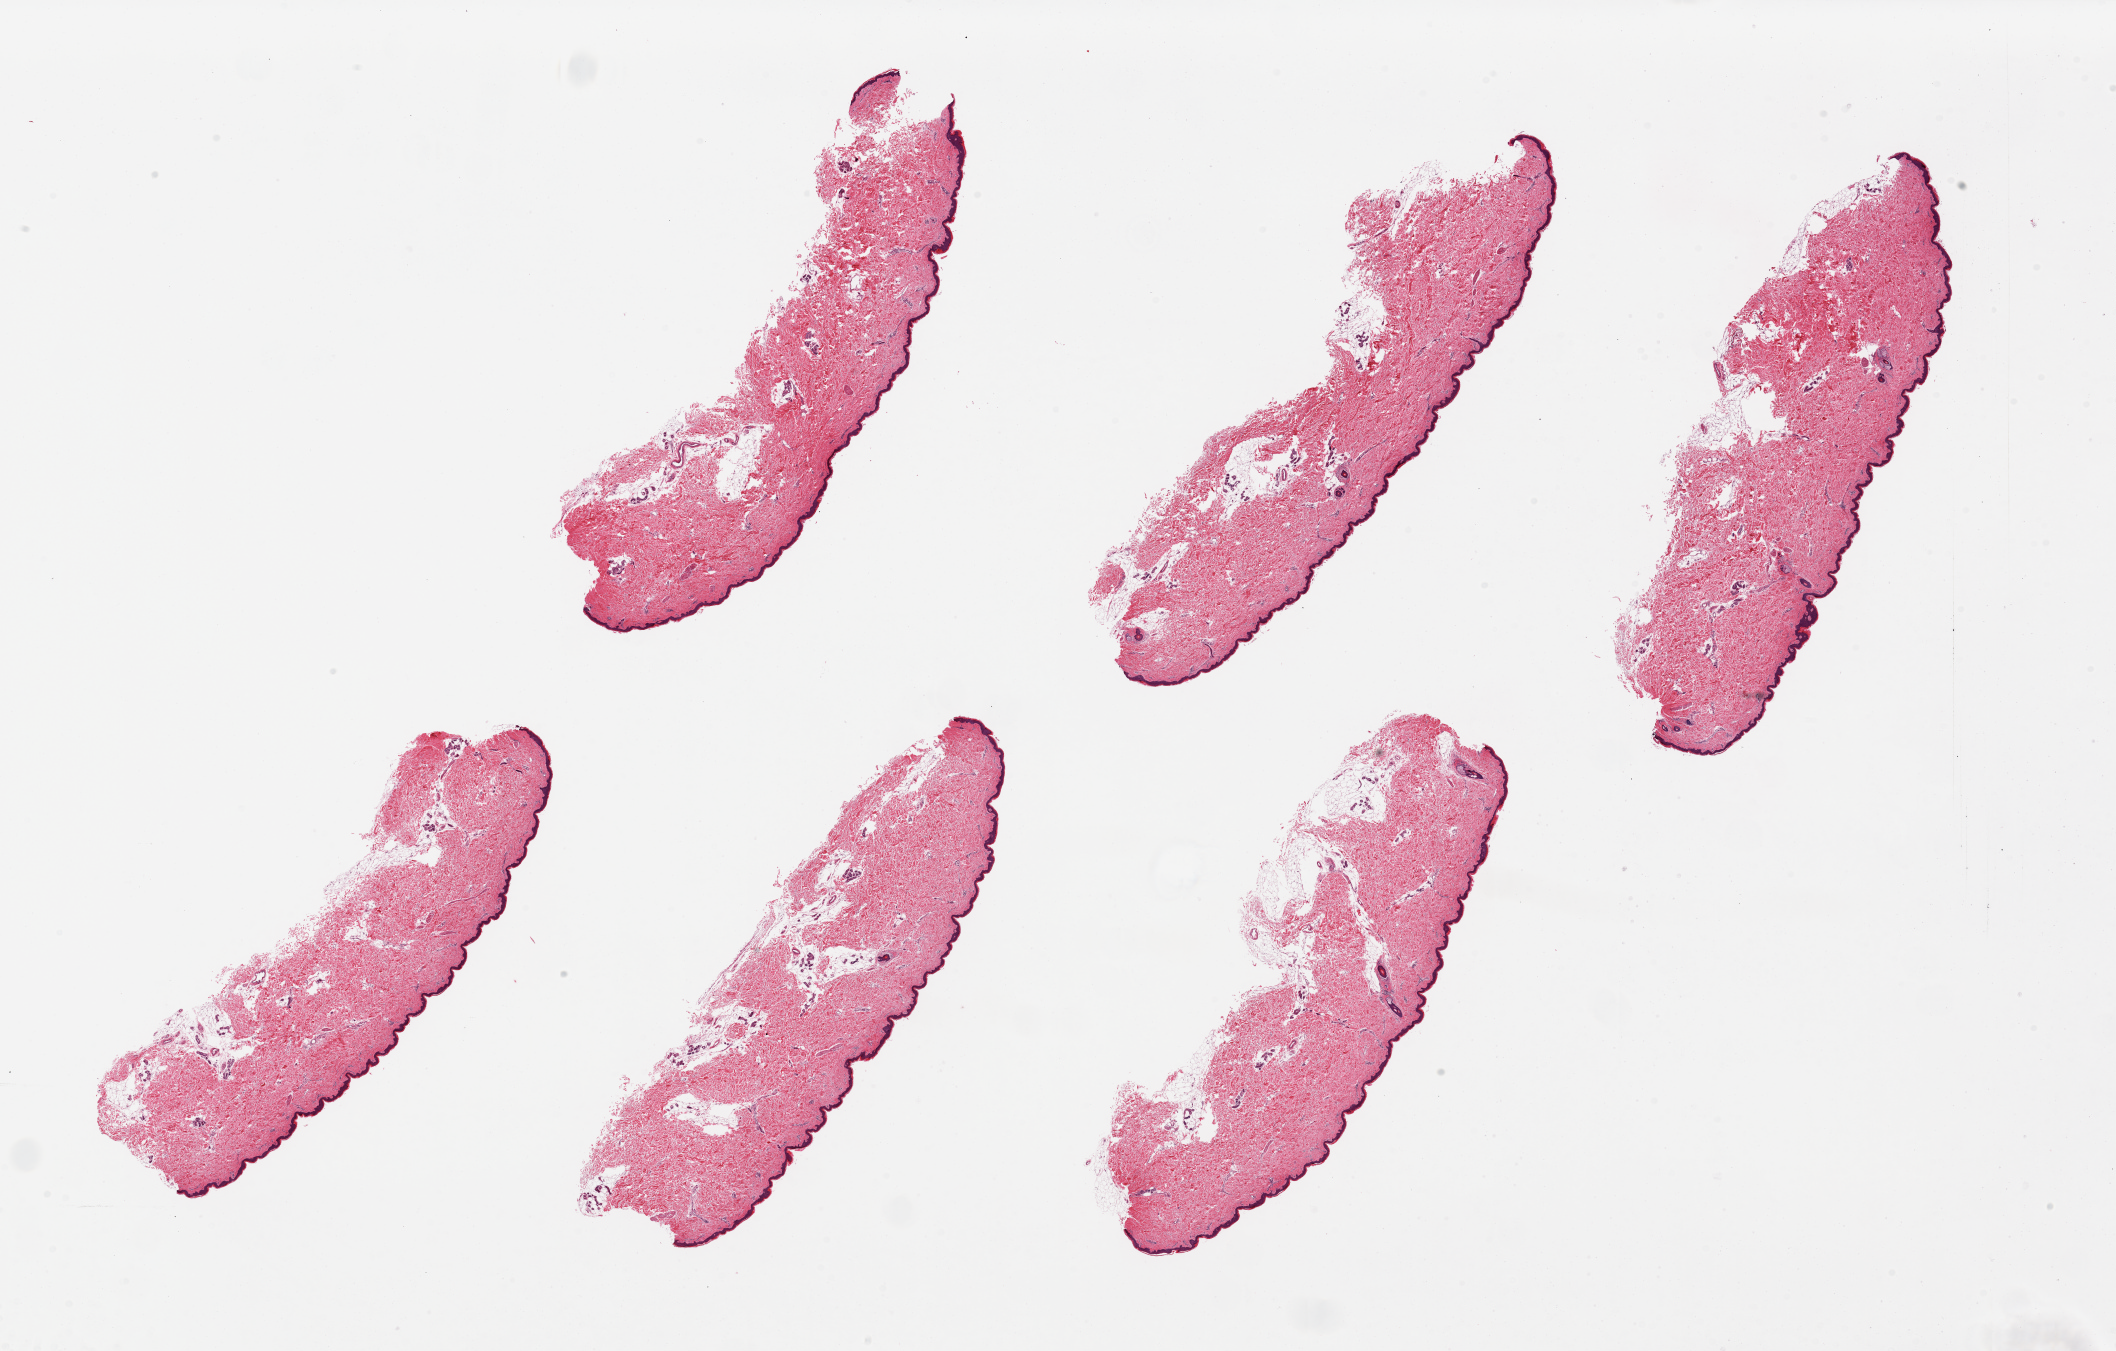
Digitized H&E-stained section — whole scanned area (about 33.5 x 21.4 mm) shown as a low-resolution overview, PAXgene-fixed, paraffin-embedded tissue, target tissue: skin of lower leg, donor tissue sample. Donor sex: female.
• reviewer comment on this tissue sample: 6 pieces. up to 10x3.5mm; 5 of 6 have well trimmed deep aspect